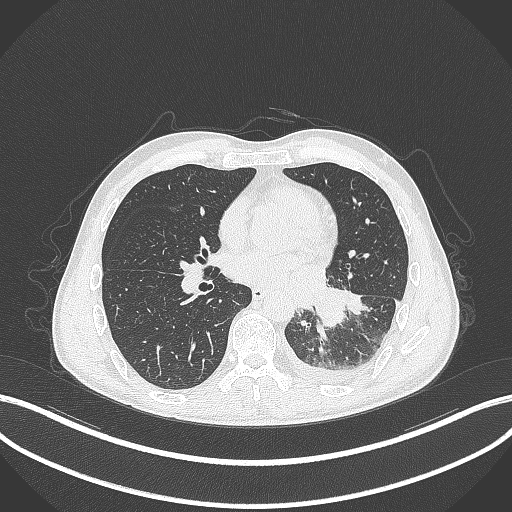
Chest CT, one axial slice; slice 140 of 295 in the series (ordered by position); 120 kVp; lung window (W 1500 / L -600 HU); 1 mm slice thickness; 512 × 512 image matrix, field of view 400 × 400 mm. Patient: male, 47 years. From the clinical record (not read from this slice): clinical TNM (as recorded): T3 N1 M1c.
Outlined on this slice (bounding box drawn by a radiologist):
- lung tumour (recorded histology: small cell carcinoma): bounding box (x1, y1, x2, y2) in pixels: (312, 285, 347, 329)